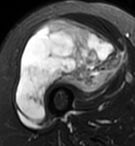
MRI of an extremity soft-tissue mass, one axial slice. Position 54 of 95 along the scan axis. T2-weighted fat-saturated. MR volume resampled by the dataset authors to the PET/CT grid (not the native acquisition matrix). 135 × 146 image matrix, field of view 132 × 143 mm. Female patient. From the clinical record (not read from this slice): histological type: pleiomorphic undifferentiated sarcoma; grade: high; site of the primary tumour: right quadricep.
Structures marked on this image (expert contour drawn on MRI and transferred to this co-registered scan by the dataset authors):
- gross tumour volume including surrounding oedema: bounding box <16,18,123,122> (left, top, right, bottom; pixels)
- gross tumour volume (mass): <16,18,123,122>